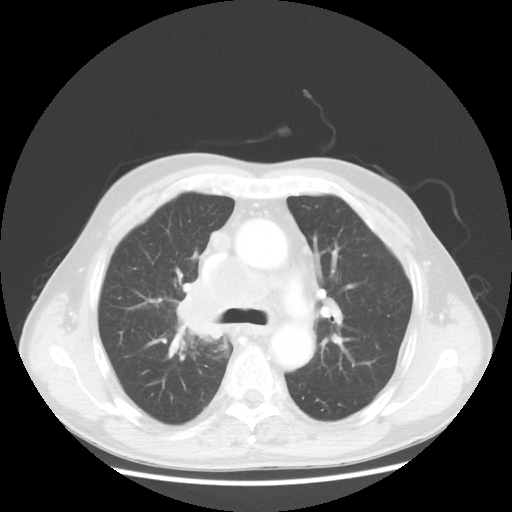
Chest CT, one axial slice. Slice 79 of 124 in the series (ordered by position). 100 kVp. Lung window (W 1500 / L -600 HU). 5 mm slice thickness. 512 × 512 image matrix. Male patient, age 64 years. Case-level facts recorded for this patient, not image findings: clinical TNM (as recorded): T3 N3 M0.
Annotated regions visible in this slice (bounding box drawn by a radiologist):
- lung tumour (recorded histology: small cell carcinoma): bounding box <174,273,231,348> (left, top, right, bottom; pixels)